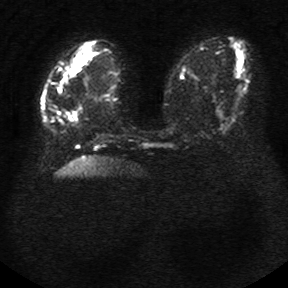
Breast MRI, one axial slice; position 11 of 34 along the scan axis; diffusion-weighted series; image 2 of 4 stored at this slice position (different b-values; order by instance number); 1.5 T; 288 × 288 image matrix, field of view 340 × 340 mm. Female patient.
Structures marked on this image (manually delineated by an expert):
- tumour on diffusion-weighted imaging: bounding box (x1, y1, x2, y2) in pixels: (64, 42, 94, 78)